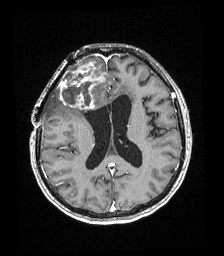
Brain MRI from a brain-tumour surgery series, one axial slice. Slice 87 of 192 in the series (ordered by position). T1-weighted post-contrast. 224 × 256 image matrix, field of view 219 × 250 mm. From the clinical record (not read from this slice): histopathology: Astrocytoma; WHO grade: 4; IDH mutation: yes.
Structures marked on this image (expert manual segmentation):
- tumour: bounding box [x1, y1, x2, y2] px = [59, 62, 105, 109]